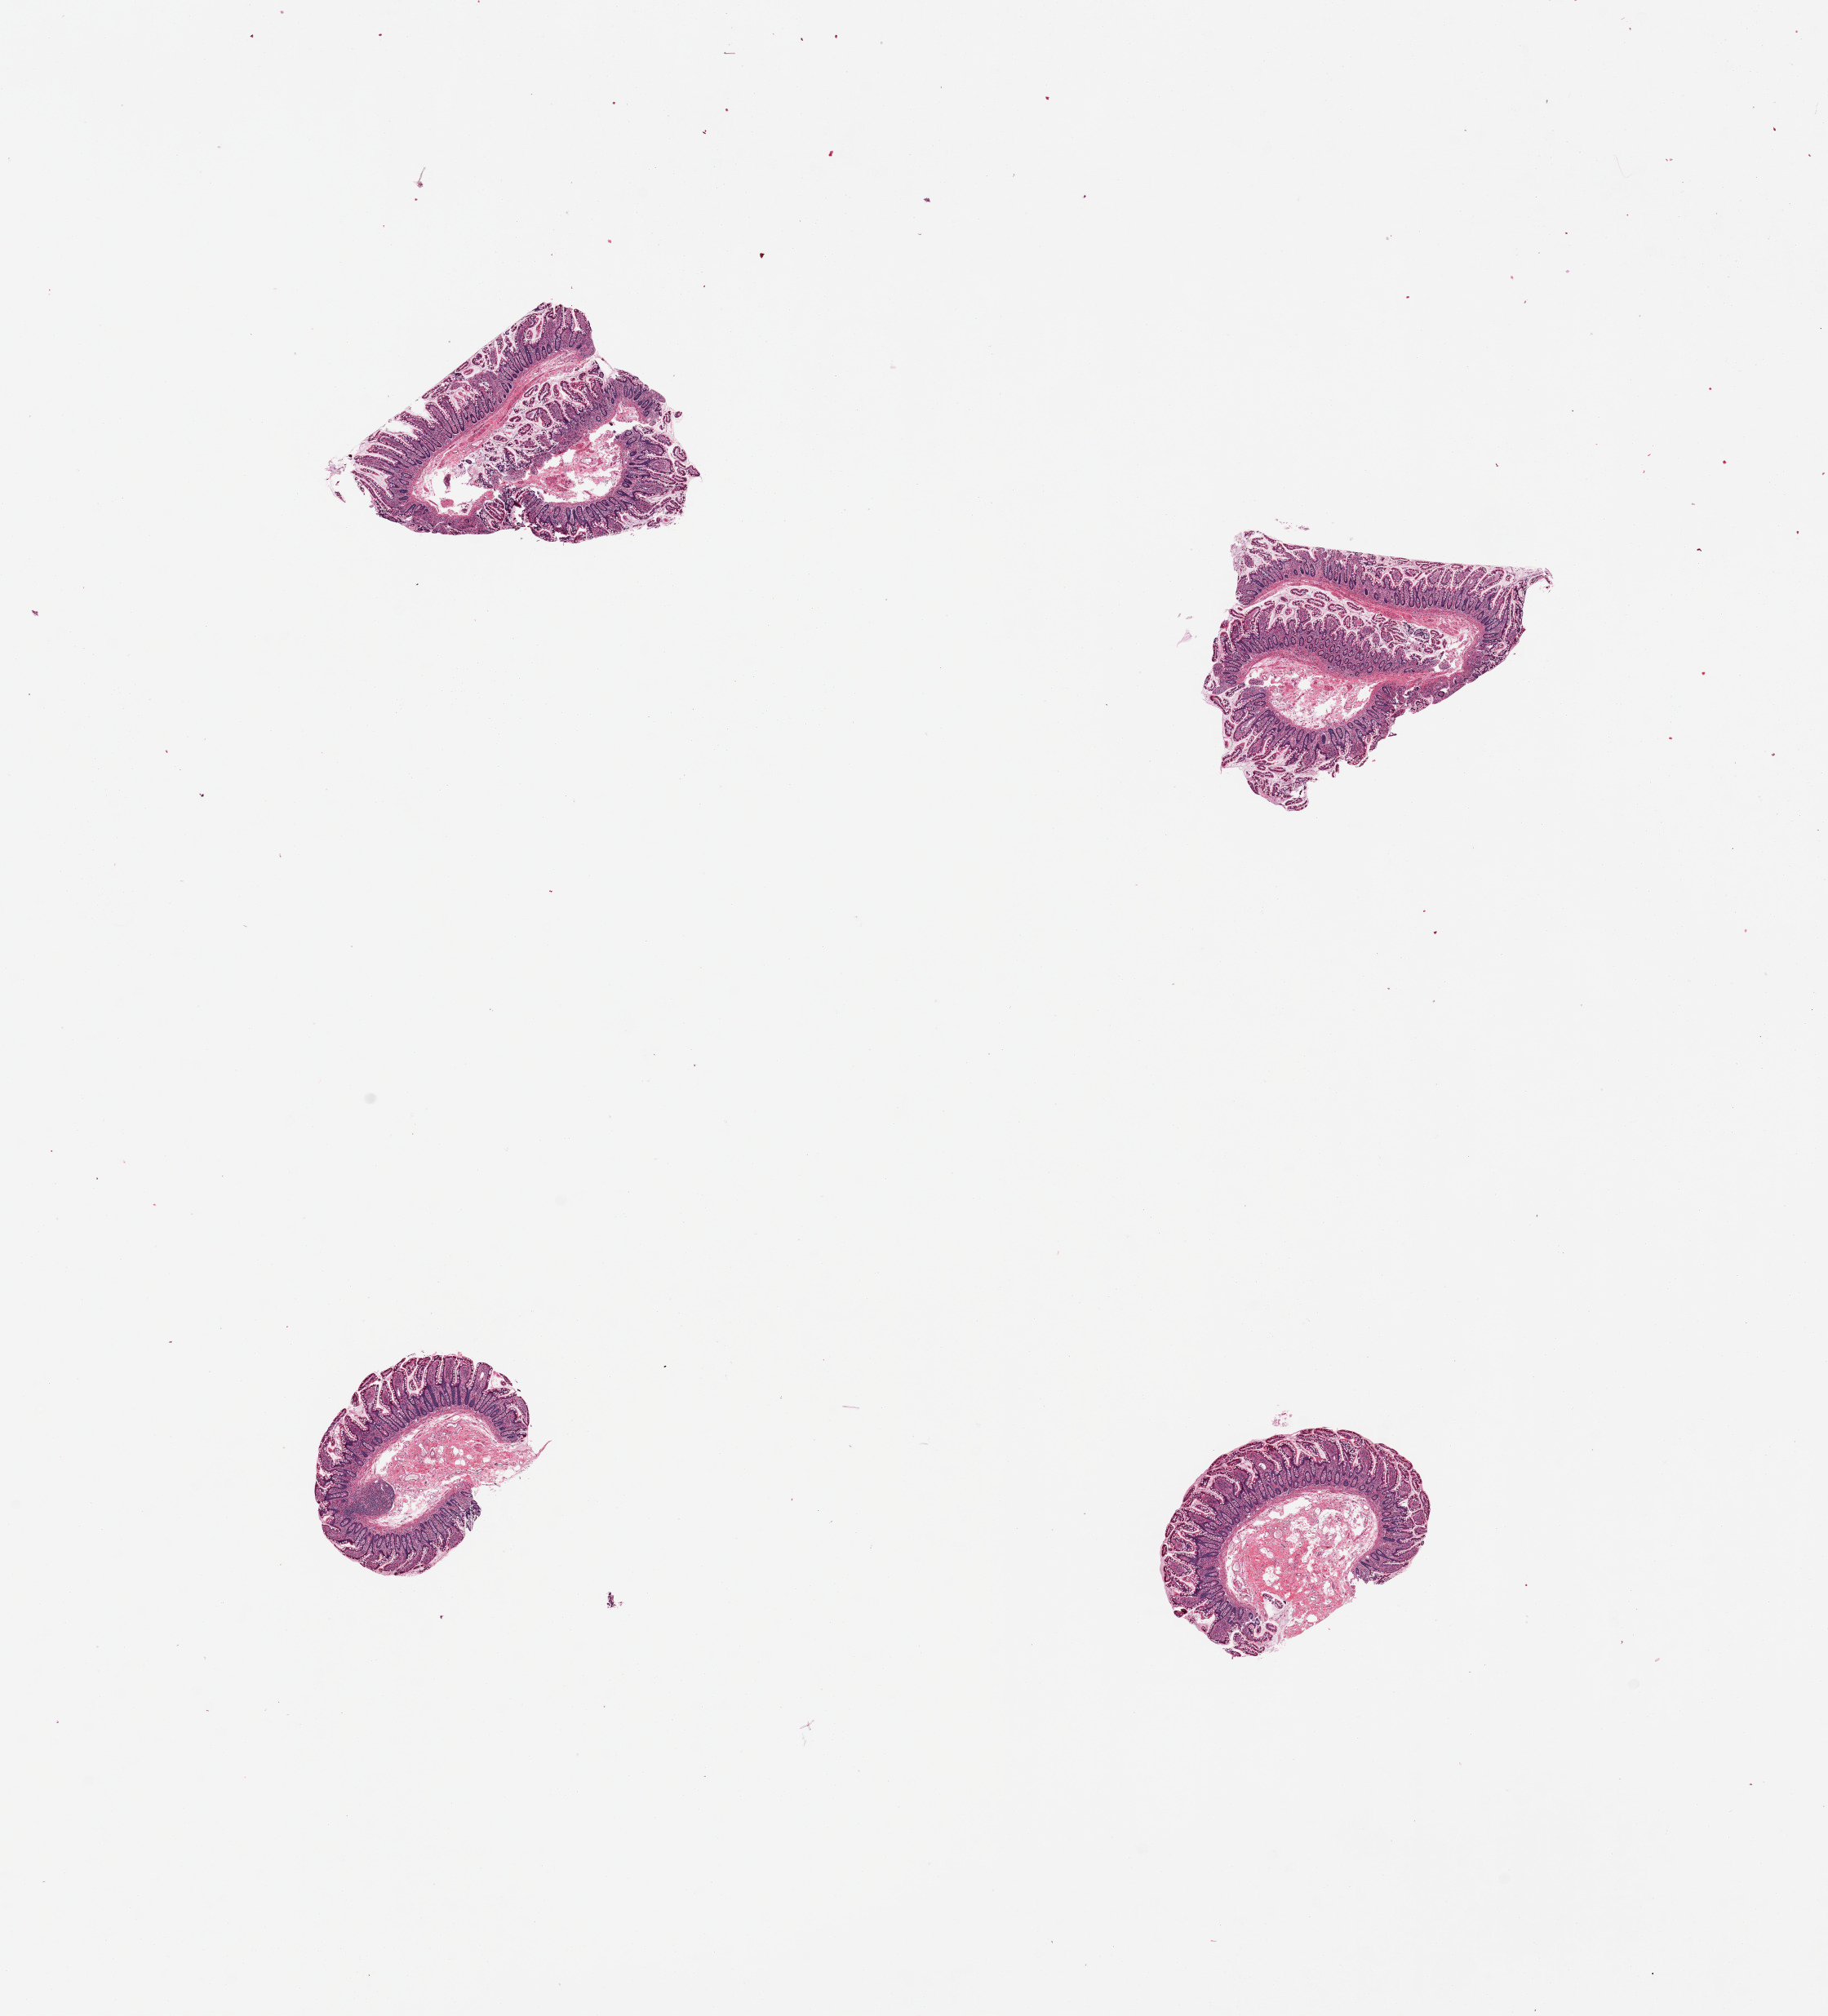
Digitized H&E-stained section — whole scanned area (about 17.7 x 19.5 mm) shown as a low-resolution overview. PAXgene-fixed paraffin-embedded (PFPE) section. Sampled site (target tissue): ileum. Donor tissue sample. Male donor.
• pathologist's review note for this sample: 4 pieces, nearly pure mucosa; lymphoid elements are ~20% of tissue, only rare aggregates